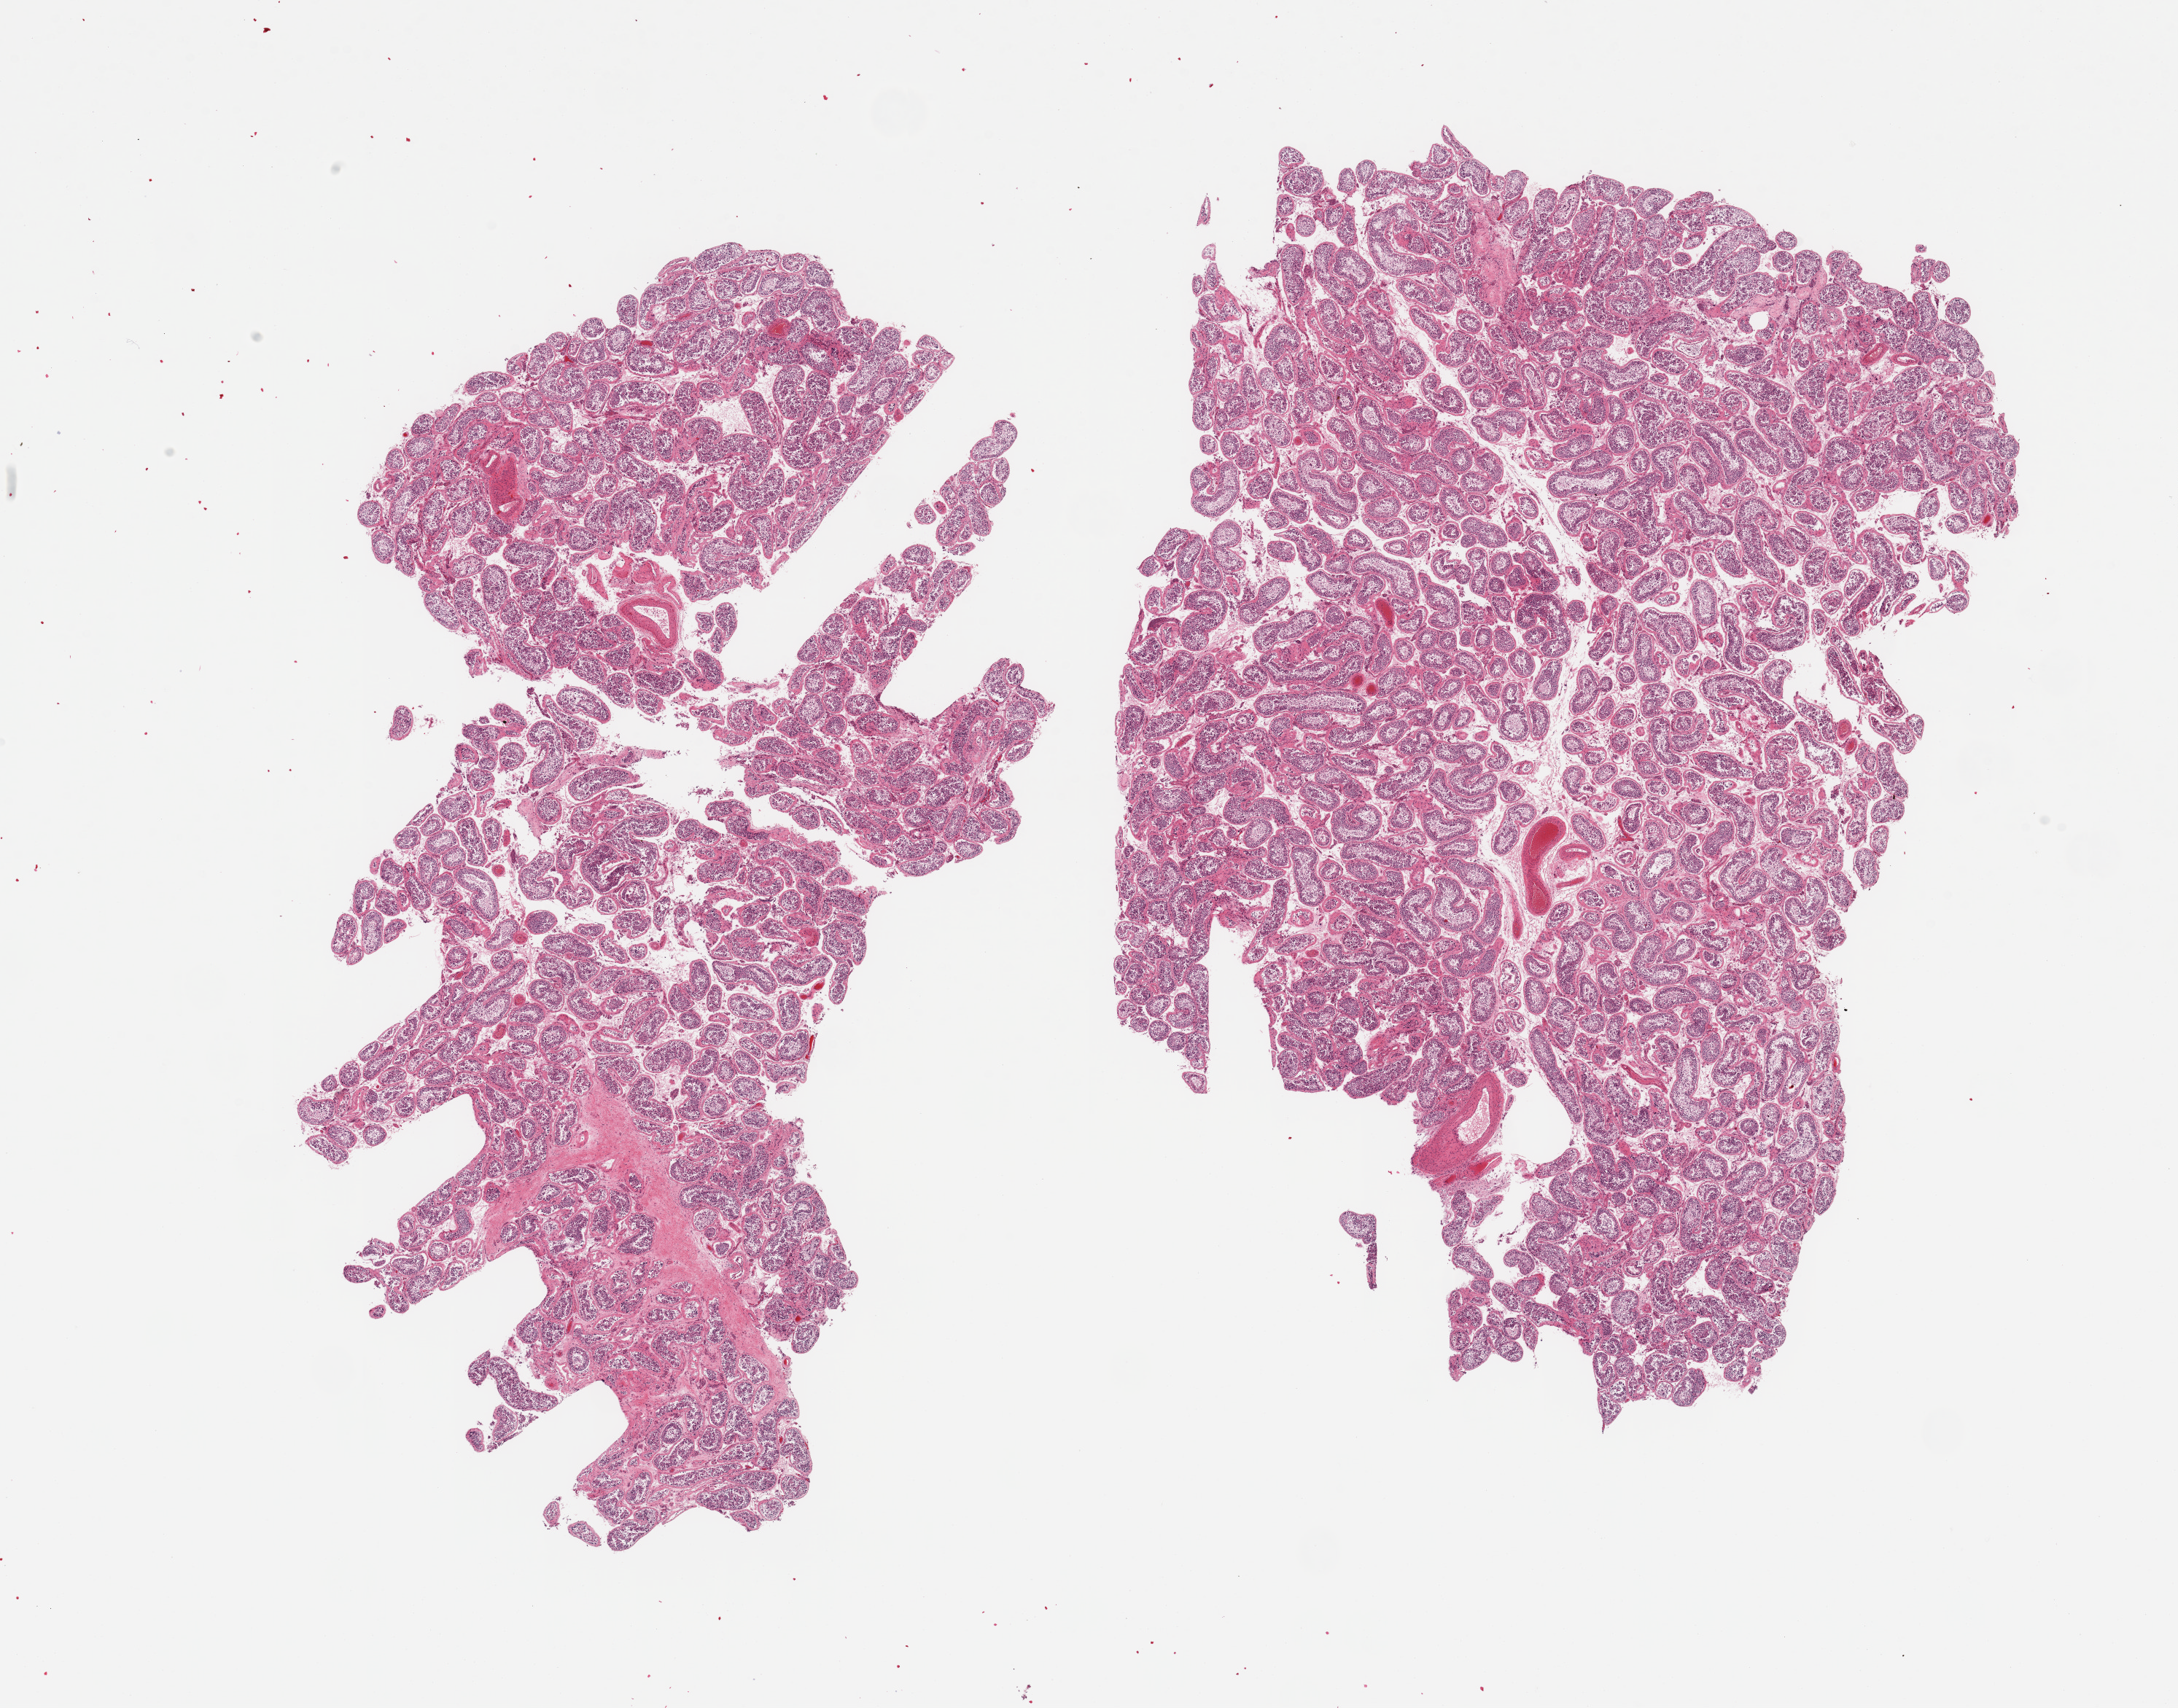
H&E whole-slide image, brightfield, shown as a low-resolution overview of the whole scanned area (about 23.6 x 18.5 mm); PAXgene-fixed paraffin-embedded (PFPE) section; target tissue: testis; tissue donor sample.
- pathologist's review note for this sample: 2 pieces, spermatogenesis appears reduced